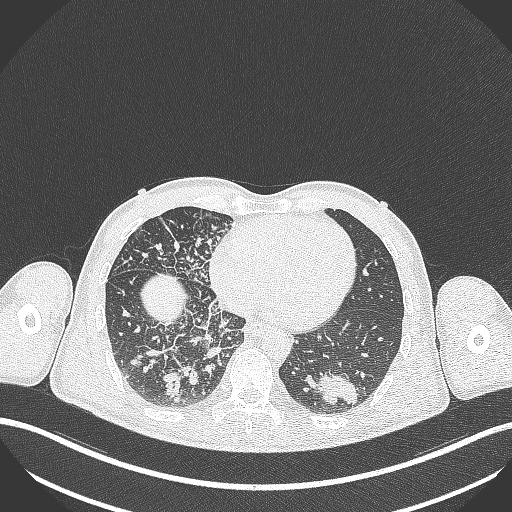
Chest CT, one axial slice; position 100 of 348 along the scan axis; reconstruction kernel B70f; lung window (W 1500 / L -600 HU); 1 mm slice thickness; 512 × 512 image matrix, field of view 400 × 400 mm. Patient: male, 49 years. Case-level facts recorded for this patient, not image findings: clinical TNM (as recorded): T2b N1 M0.
Structures marked on this image (bounding box drawn by a radiologist):
- lung tumour (recorded histology: adenocarcinoma): bounding box (x1, y1, x2, y2) in pixels: (318, 369, 359, 409)